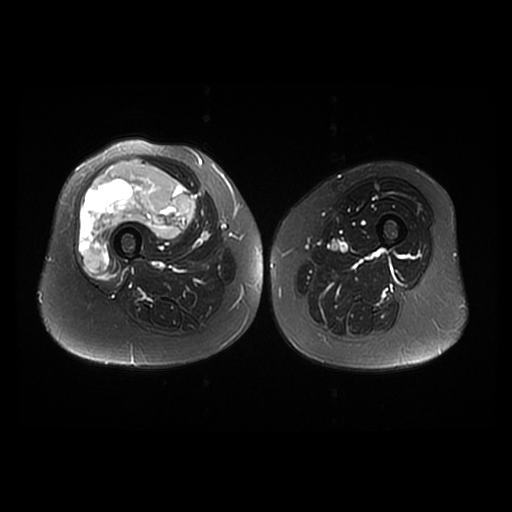
MRI of an extremity soft-tissue mass, one axial slice. Position 18 of 42 along the scan axis. T2-weighted fat-saturated. 6 mm slice thickness. 512 × 512 image matrix, field of view 440 × 440 mm. Female patient. Case-level facts recorded for this patient, not image findings: histological type: pleiomorphic undifferentiated sarcoma; grade: high; site of the primary tumour: right quadricep.
Outlined on this slice (expert manual segmentation):
- gross tumour volume including surrounding oedema: bounding box <79,159,195,274> (left, top, right, bottom; pixels)
- gross tumour volume (mass): <79,159,195,274>